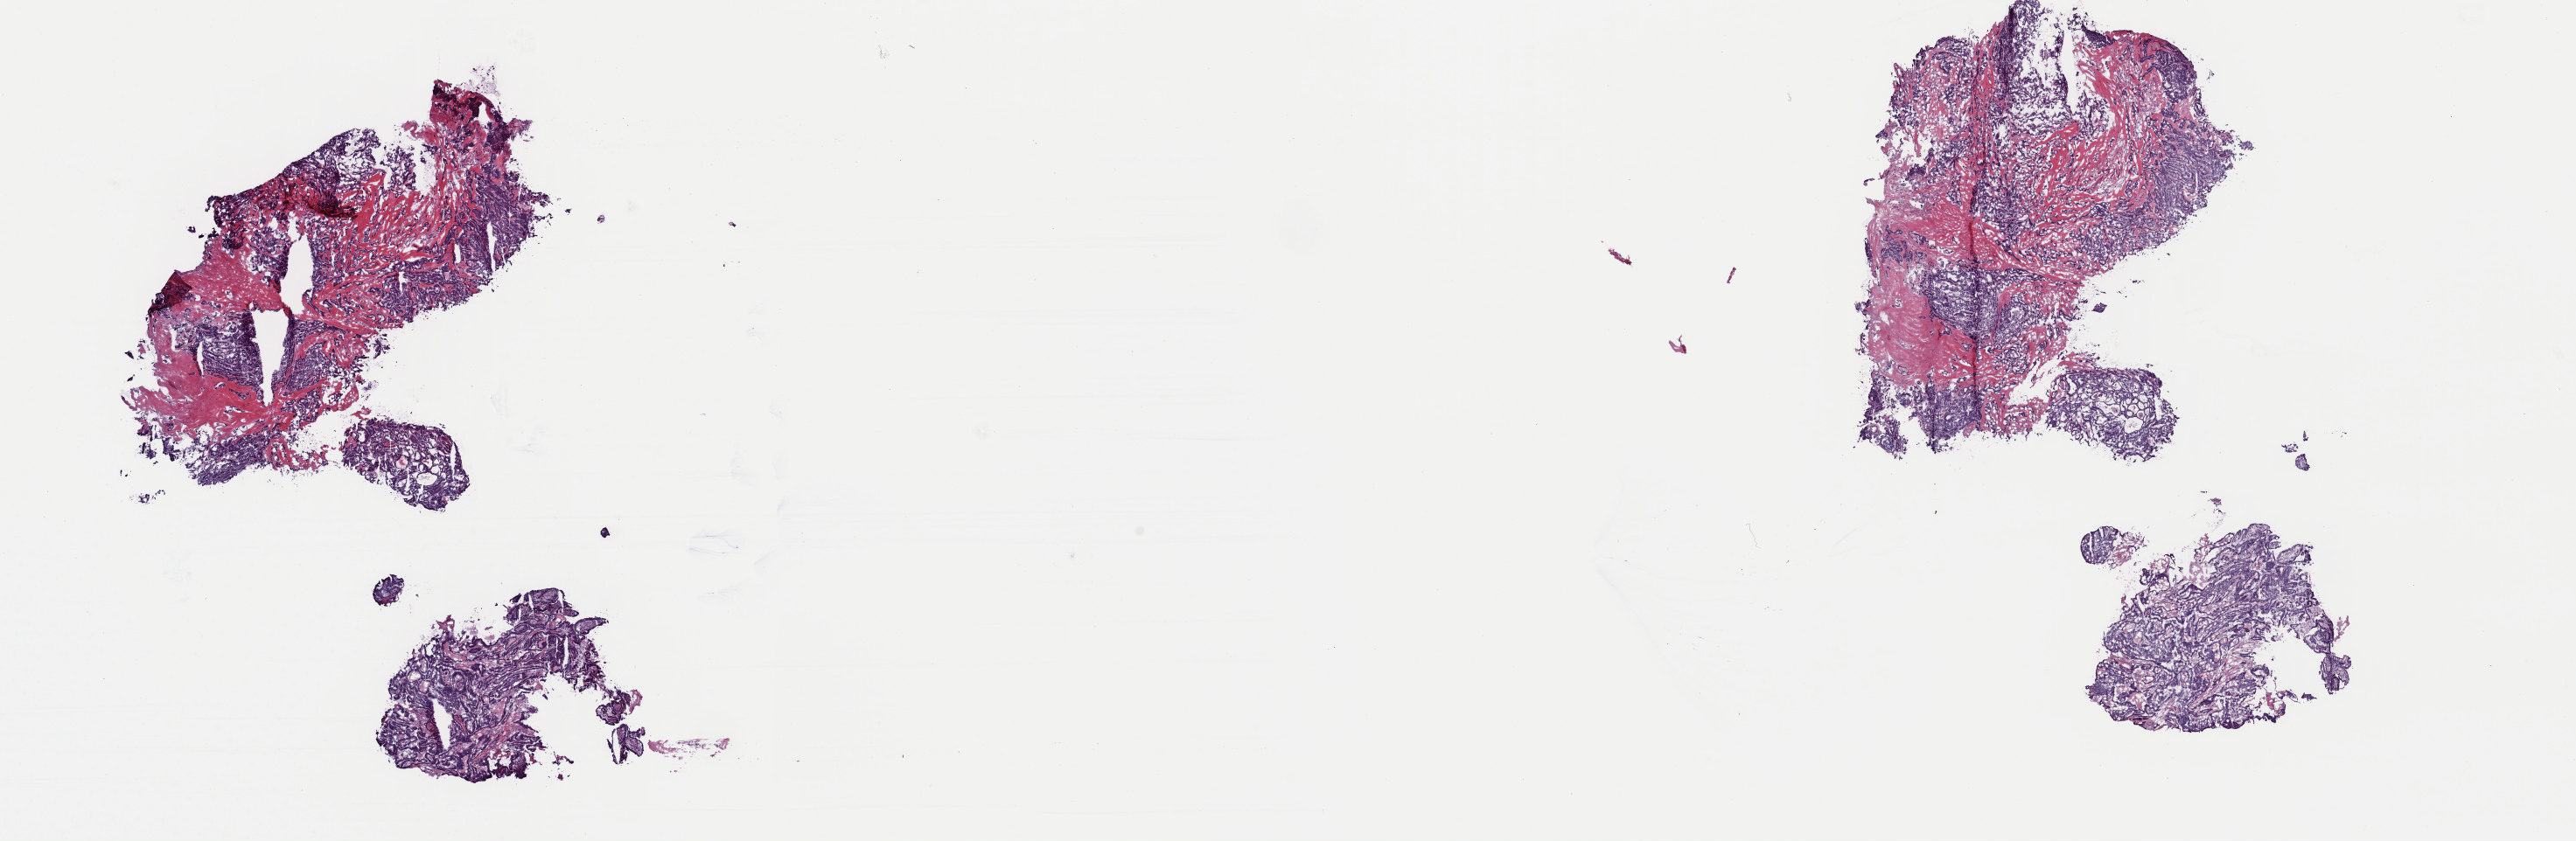
Whole-slide histology image, H&E — a low-resolution overview of the entire scanned area, about 23.3 x 7.6 mm (slide scanned at 40x), frozen section from the top of the tissue portion, thyroid, primary tumour sample. Female, age 59 years at initial diagnosis. Pathologist review of this section (percent, as recorded): tumour cells 50%, tumour nuclei 75%, normal cells 0%, stromal cells 50%, necrosis 0%. Infiltration values recorded for this section: lymphocyte infiltration 2%, monocyte infiltration 1%, neutrophil infiltration 0%.
* AJCC pathologic stage: IVA (7th edition)
* diagnosis: Papillary adenocarcinoma, NOS